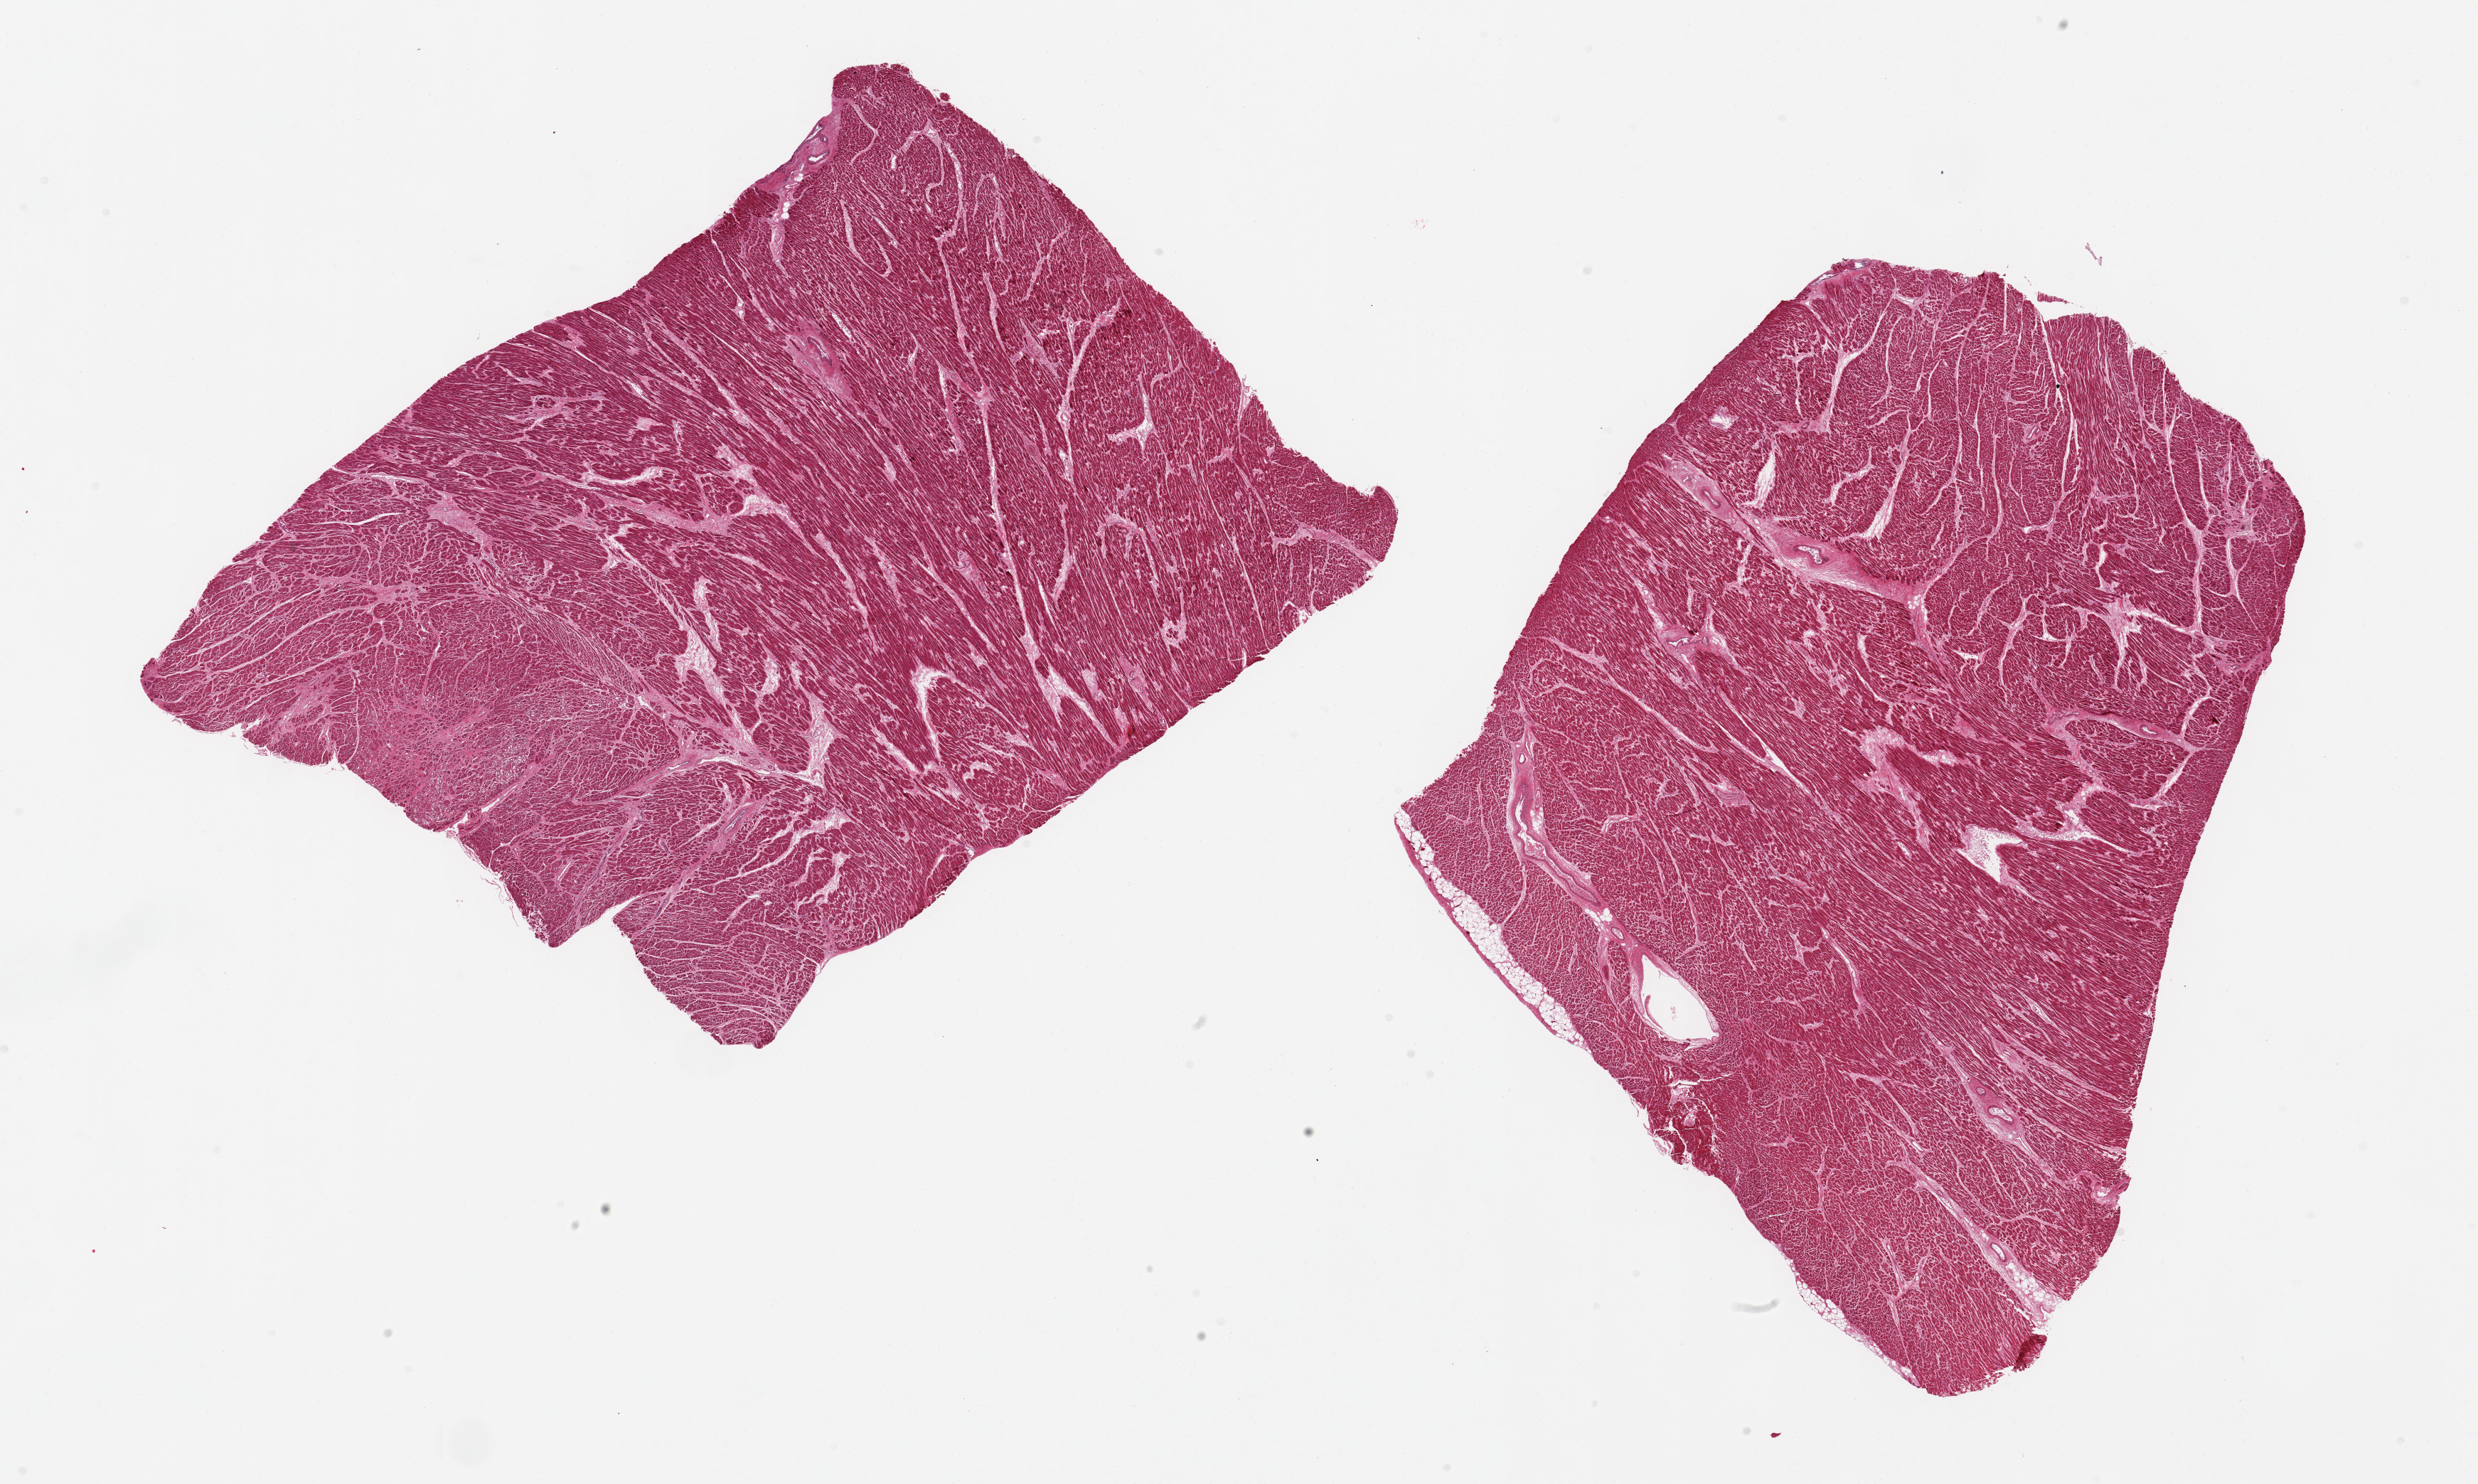
Whole-slide image, haematoxylin and eosin stain, a low-resolution overview of the entire scanned area, about 27.6 x 16.5 mm (acquisition: 20x scan). PAXgene-fixed, paraffin-embedded tissue. Section of heart (target tissue). Tissue donor sample. Donor: male.
Review note (as recorded): 2 pieces, mild interstitial fibrosis/chronic ischemic change.